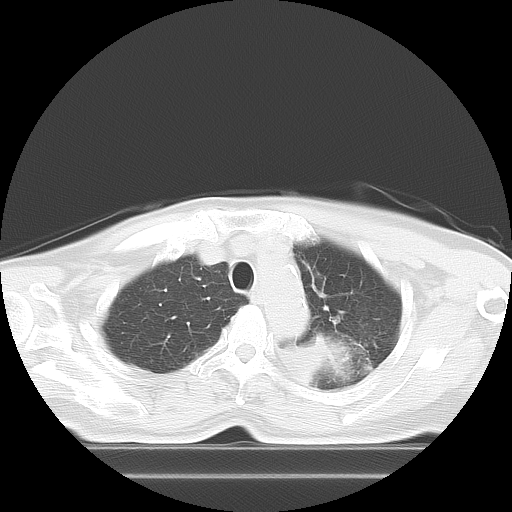
Chest CT, one axial slice. Slice 11 of 21 in the series (ordered by position). Reconstruction kernel LUNG. Lung window (W 1500 / L -600 HU). 5 mm slice thickness. 512 × 512 image matrix, field of view 350 × 350 mm. Patient: female, 74 years. Case-level facts recorded for this patient, not image findings: clinical TNM (as recorded): T3 N1 M1c; histopathological grade: G3.
Outlined on this slice (bounding box drawn by a radiologist):
- lung tumour (recorded histology: small cell carcinoma): bounding box (x1, y1, x2, y2) in pixels: (303, 330, 358, 382)